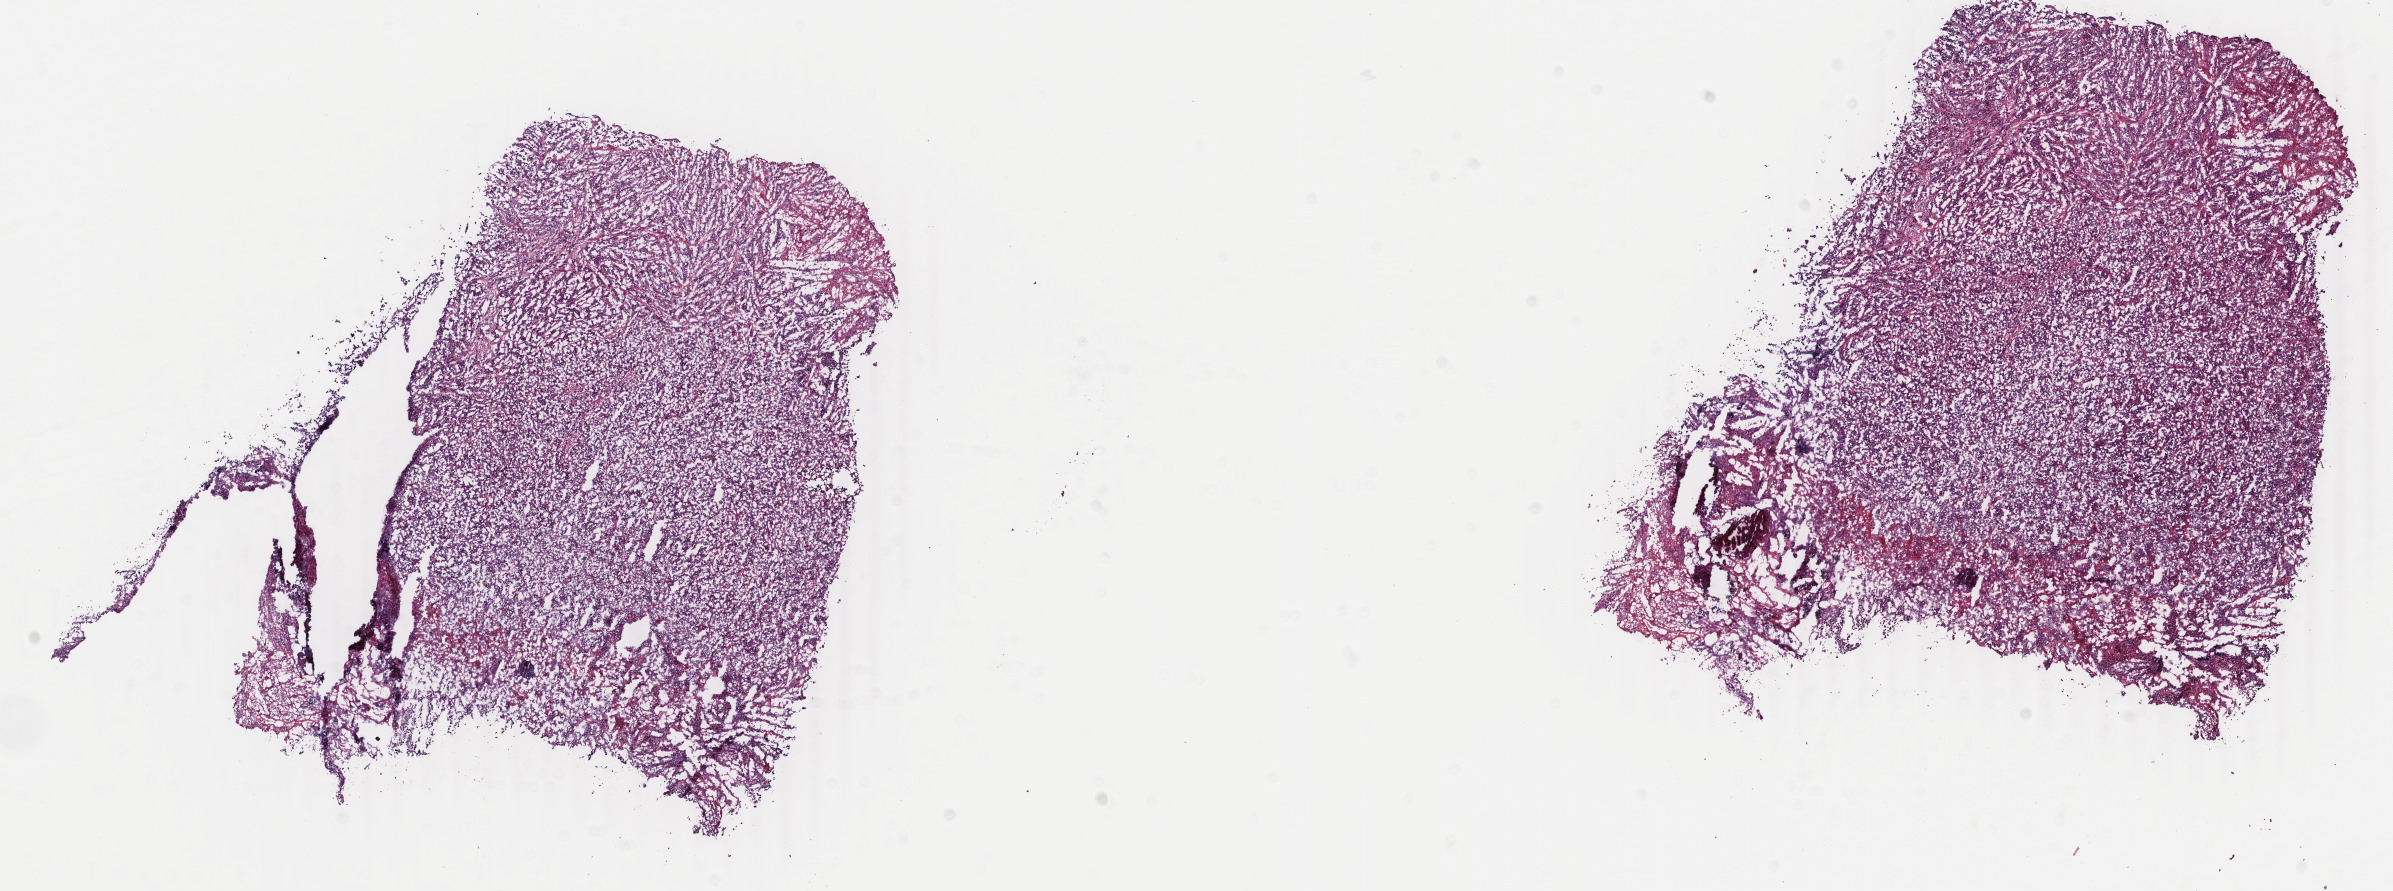
H&E-stained whole-slide image — low-resolution overview of the scanned area, about 19.0 x 7.1 mm (acquisition: 40x scan); frozen section; bladder, primary tumour sample. Patient: male, age at initial diagnosis 83 years. Histologic grade: high grade. Slide review estimates, as recorded: tumour cells 85%, tumour nuclei 85%, normal cells 0%, stromal cells 3%, necrosis 12%. Infiltration values recorded for this section: lymphocyte infiltration 0%, monocyte infiltration 0%, neutrophil infiltration 0%.
Histologic diagnosis: Transitional cell carcinoma. AJCC pathologic stage: IV.